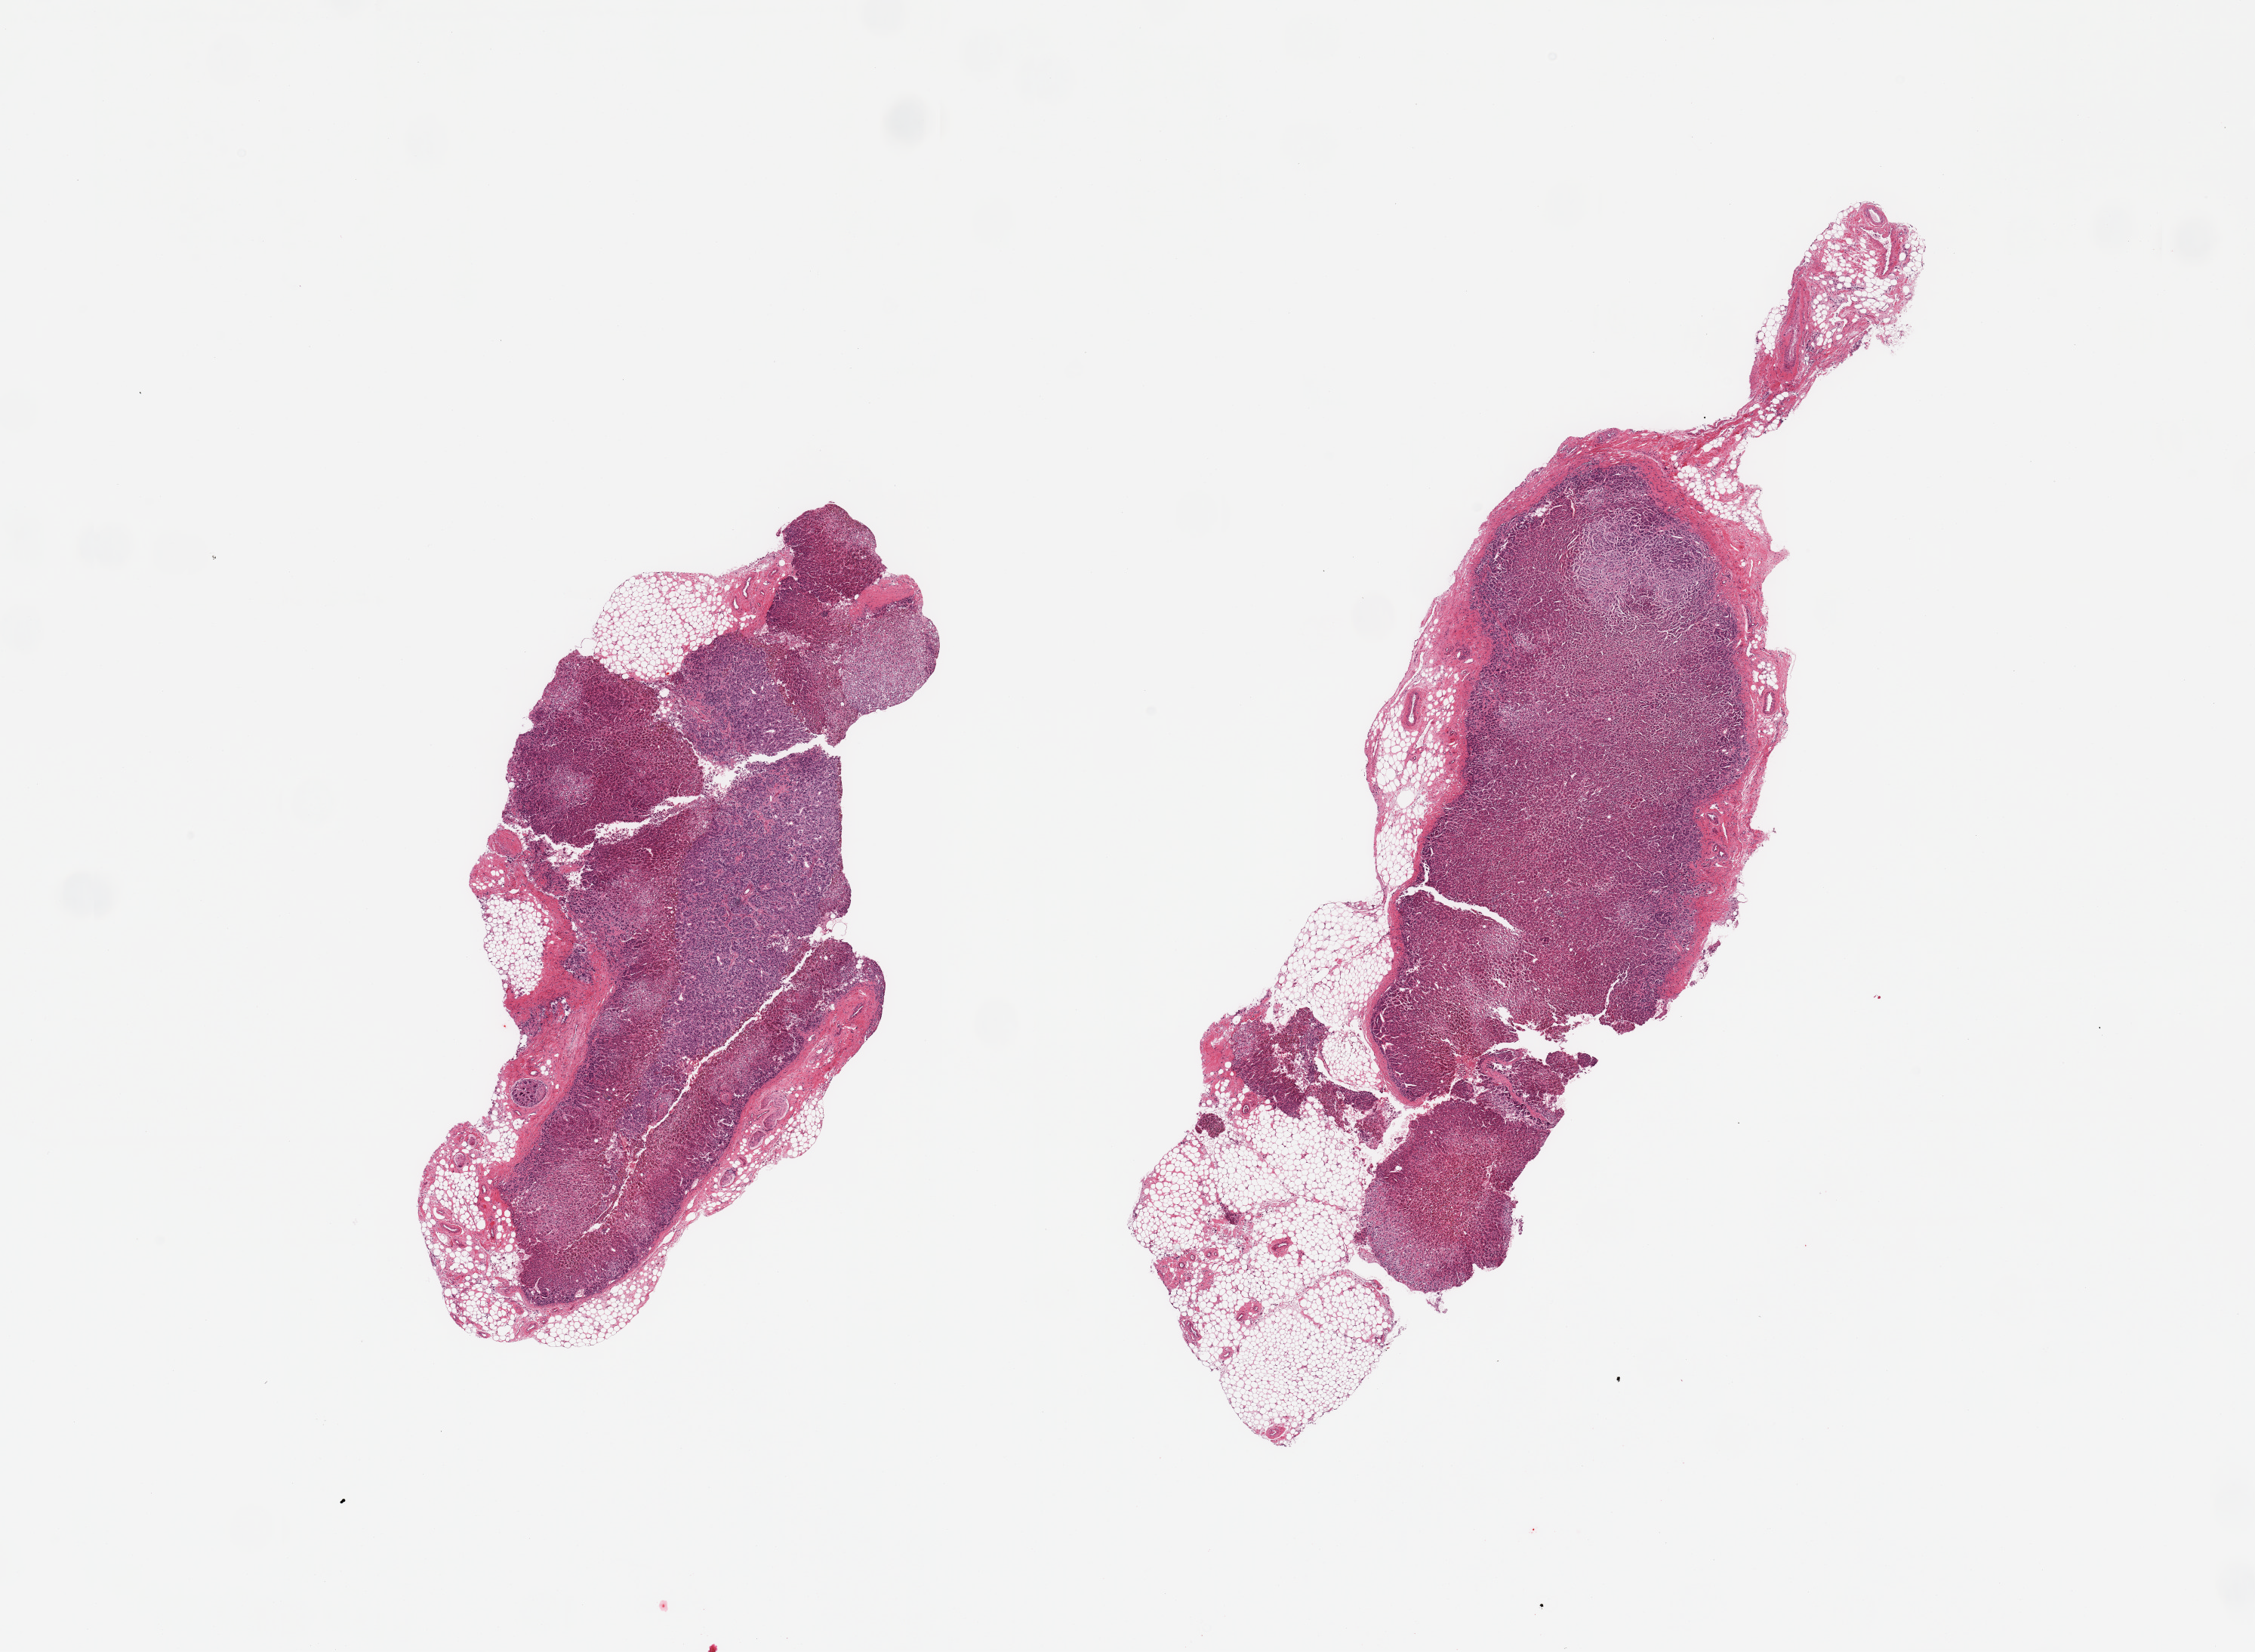
Haematoxylin and eosin whole-slide image, brightfield, a low-resolution overview of the entire scanned area, about 23.6 x 17.3 mm (slide scanned at 20x). PAXgene-fixed, paraffin-embedded tissue. Sampled site (target tissue): adrenal gland. Donor tissue sample. Donor sex: male.
Reviewer comment on this tissue sample: 2 pieces; 30% external fat.